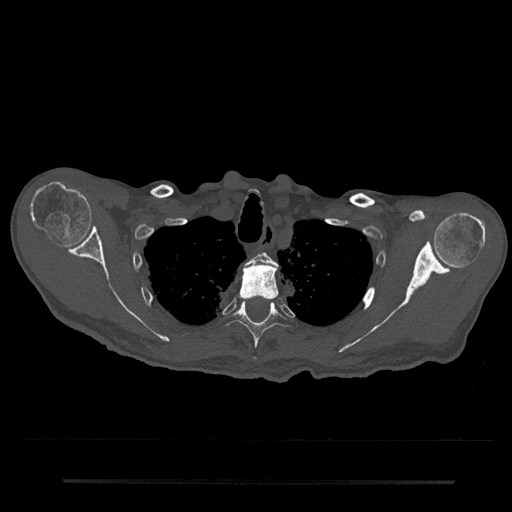
CT including the spine, one axial slice; position 640 of 797 along the scan axis; bone window (W 1800 / L 400 HU); 0.5 mm slice thickness; 512 × 512 image matrix, field of view 427 × 427 mm. Patient: male, 74 years. Case-level facts recorded for this patient, not image findings: primary cancer: prostate.
Structures marked on this image (semi-automatic segmentation, software-assisted and operator-edited):
- T2 vertebra: bounding box [x1, y1, x2, y2] px = [245, 253, 277, 268]
- T3 vertebra: [239, 263, 279, 301]
- T4 vertebra: [224, 299, 289, 361]